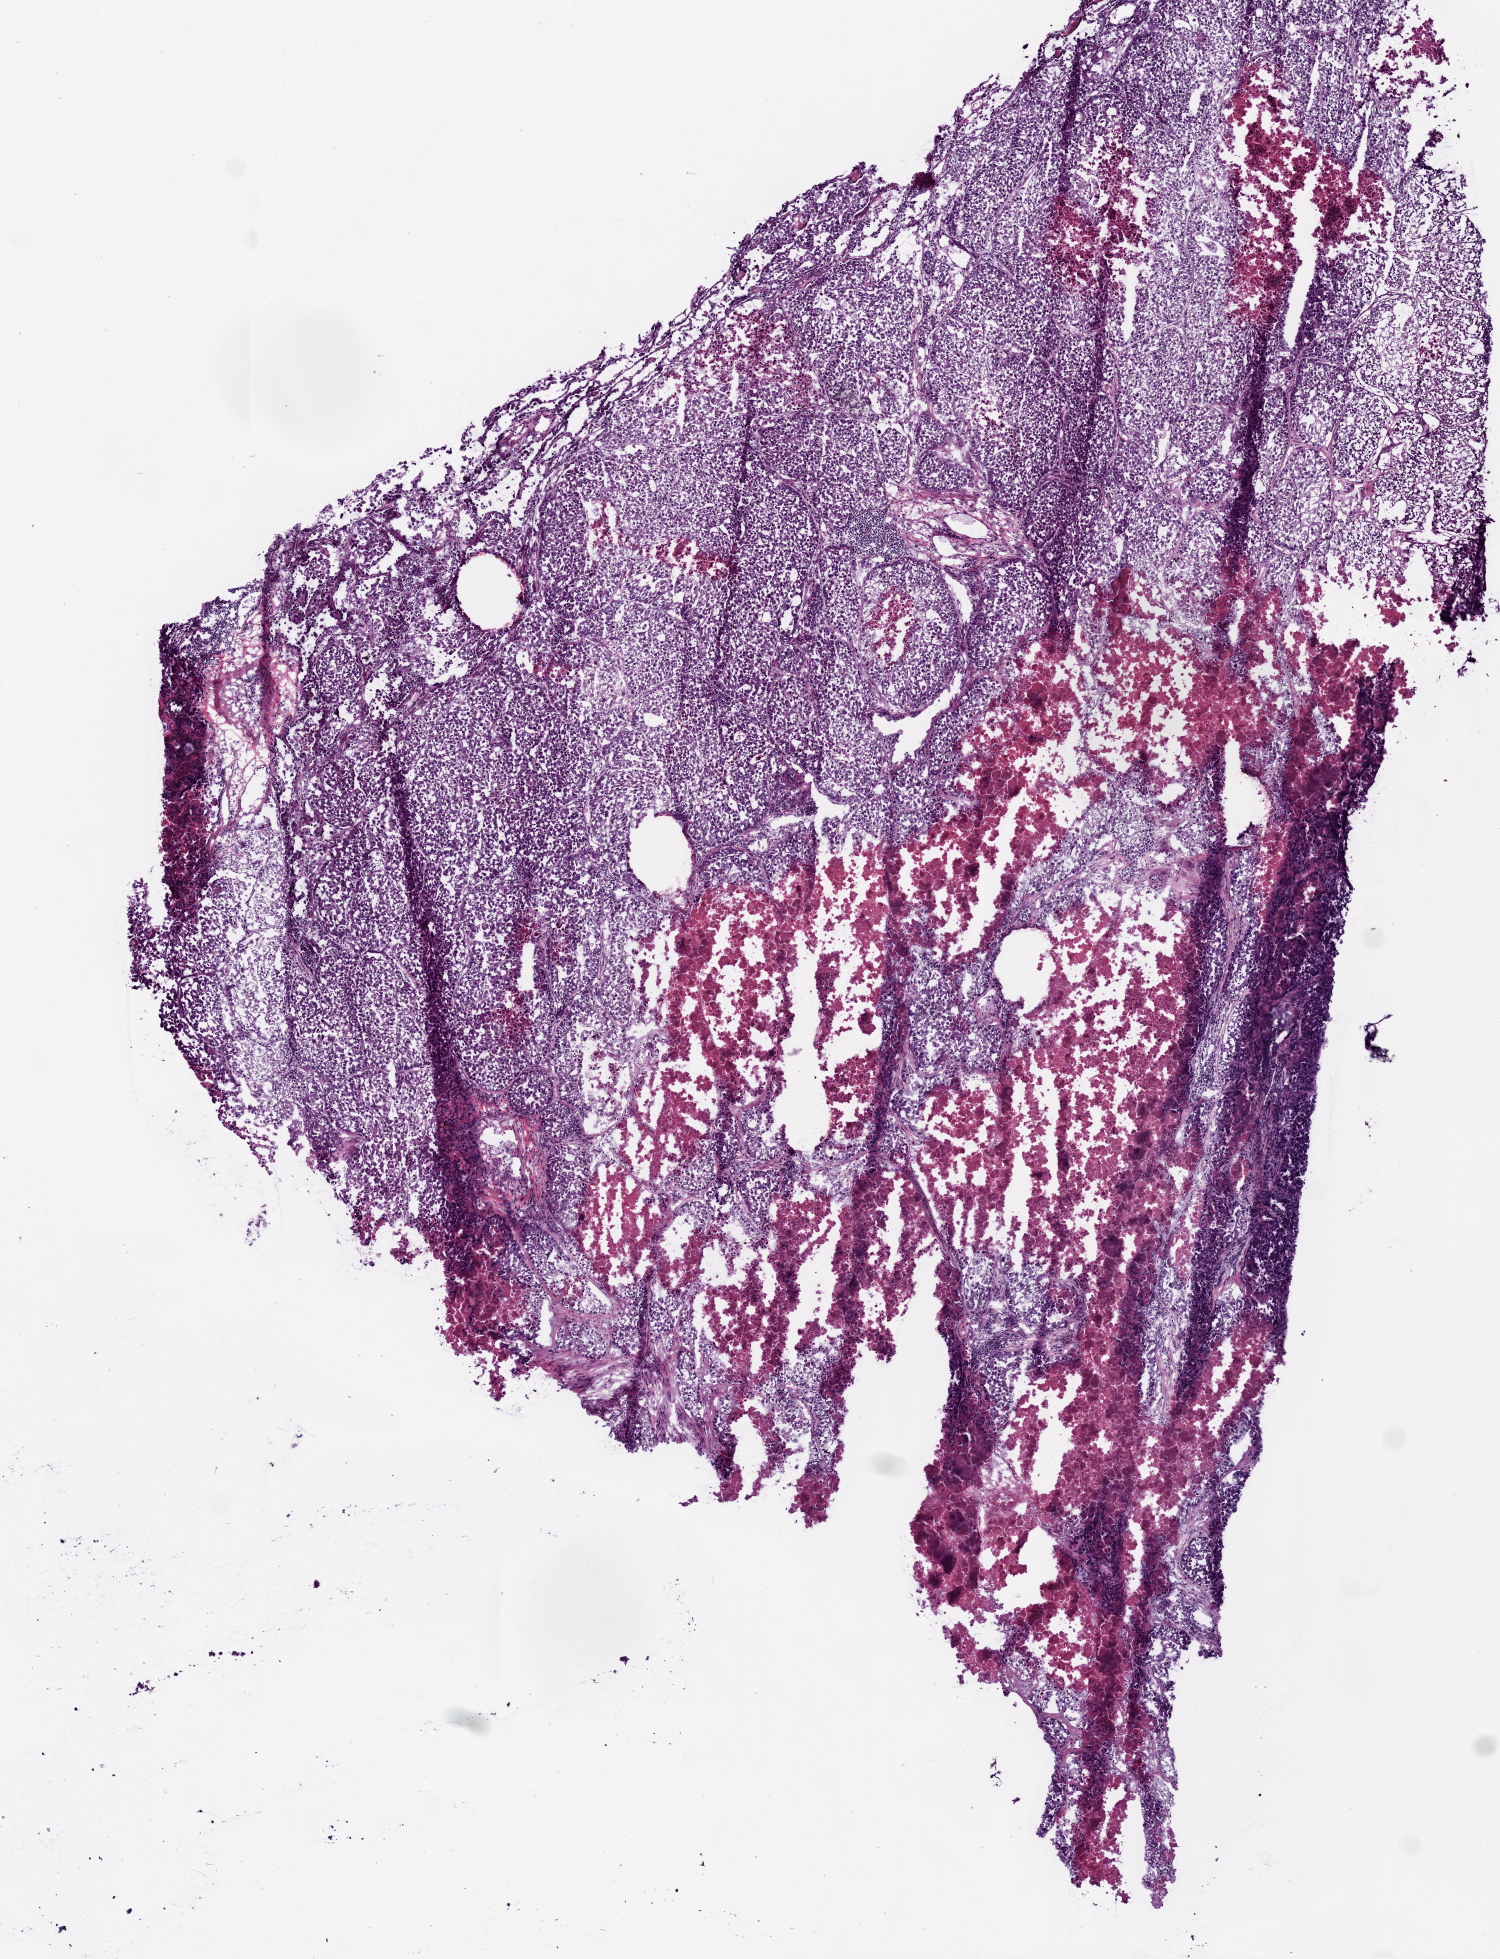
Digitized H&E-stained tissue section (whole slide) — shown as a low-resolution overview of the whole scanned area (about 6.0 x 7.9 mm, from a 20x scan), frozen section from the top of the tissue portion, sample: primary tumour, lung. Patient: male, age at initial diagnosis 62 years. Composition of this section per pathologist review: tumour cells 95%, tumour nuclei 85%.
Histologic diagnosis: Adenocarcinoma, NOS (lower lobe, lung).